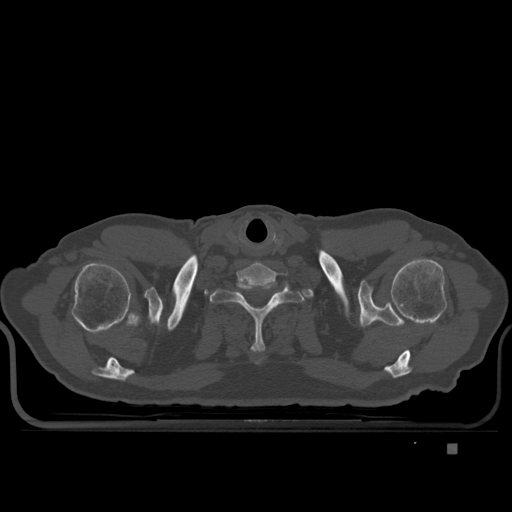
CT including the spine, one axial slice. Position 327 of 435 along the scan axis. Bone window (W 1800 / L 400 HU). 1.5 mm slice thickness. 512 × 512 image matrix. Male patient, age 73 years. Case-level facts recorded for this patient, not image findings: primary cancer: skin.
Outlined on this slice (semi-automatically segmented with operator editing):
- T1 vertebra: bounding box (x1, y1, x2, y2) in pixels: (209, 277, 304, 353)